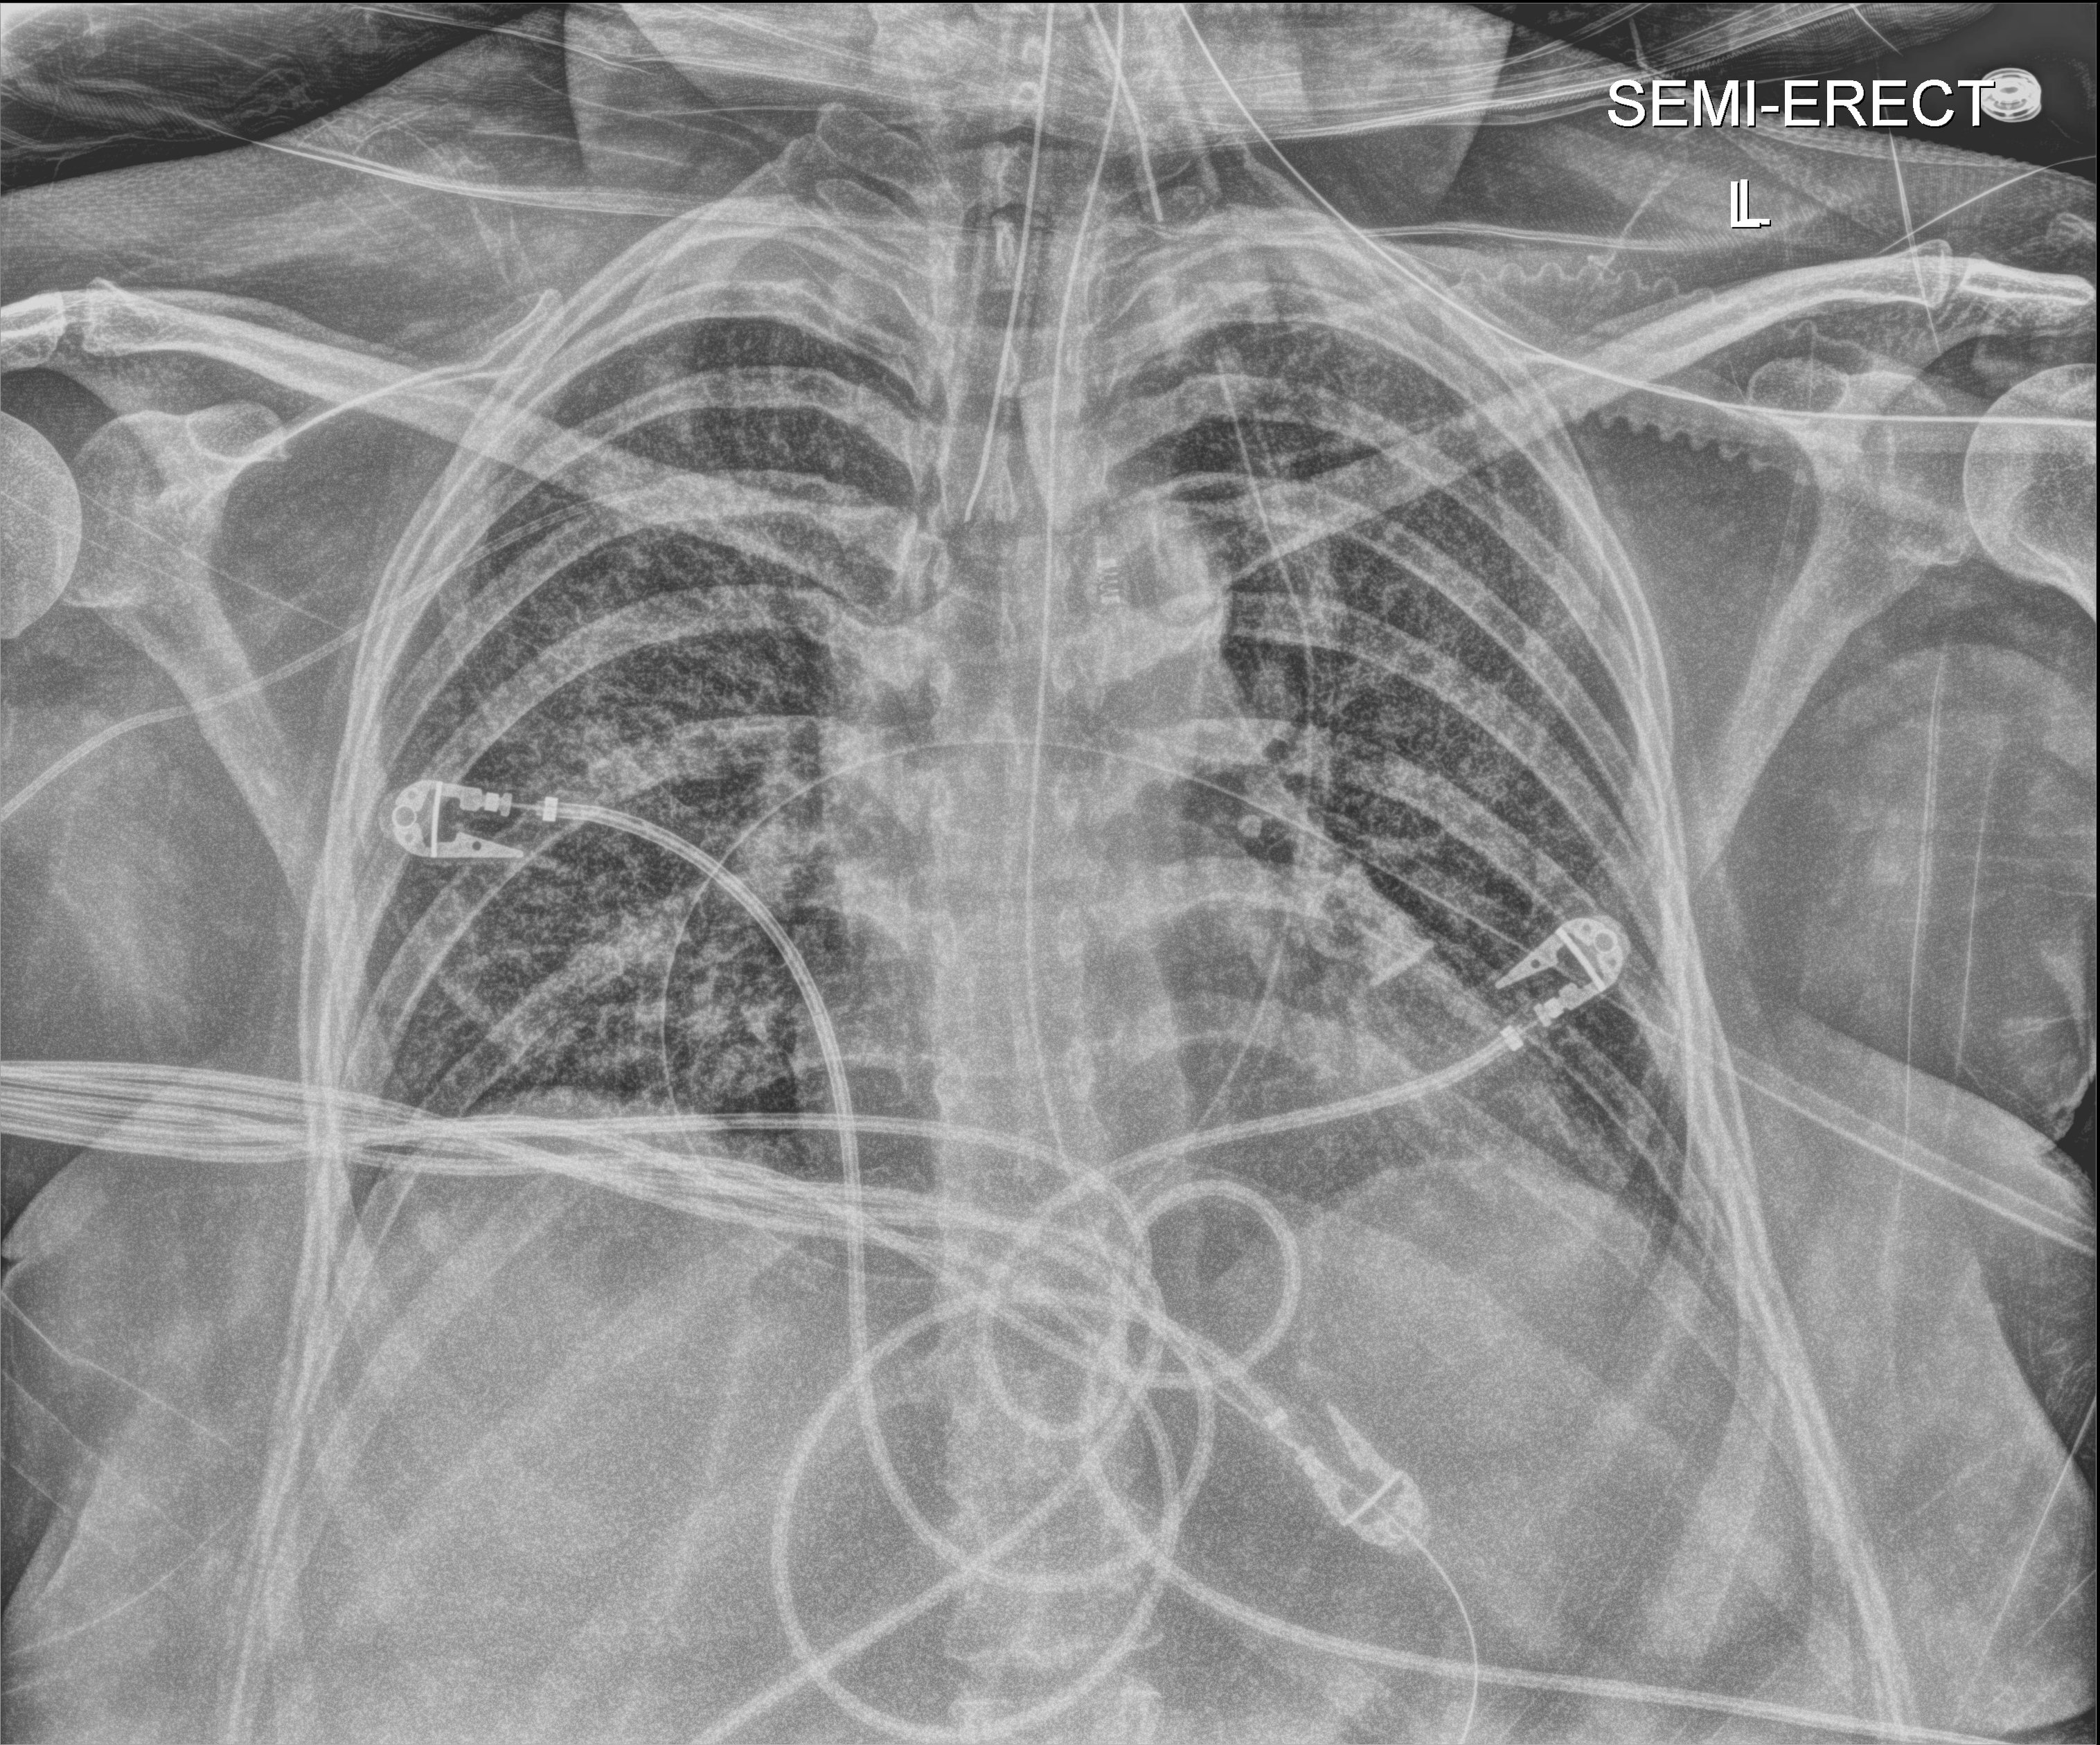
Portable chest radiograph. Patient hospitalised with COVID-19; female, aged 18–59 years.
Hospital-stay facts (about this admission, not read from this image; timing relative to this image not recorded): admitted to intensive care during this hospital stay: yes; hypertension (admission record): no.